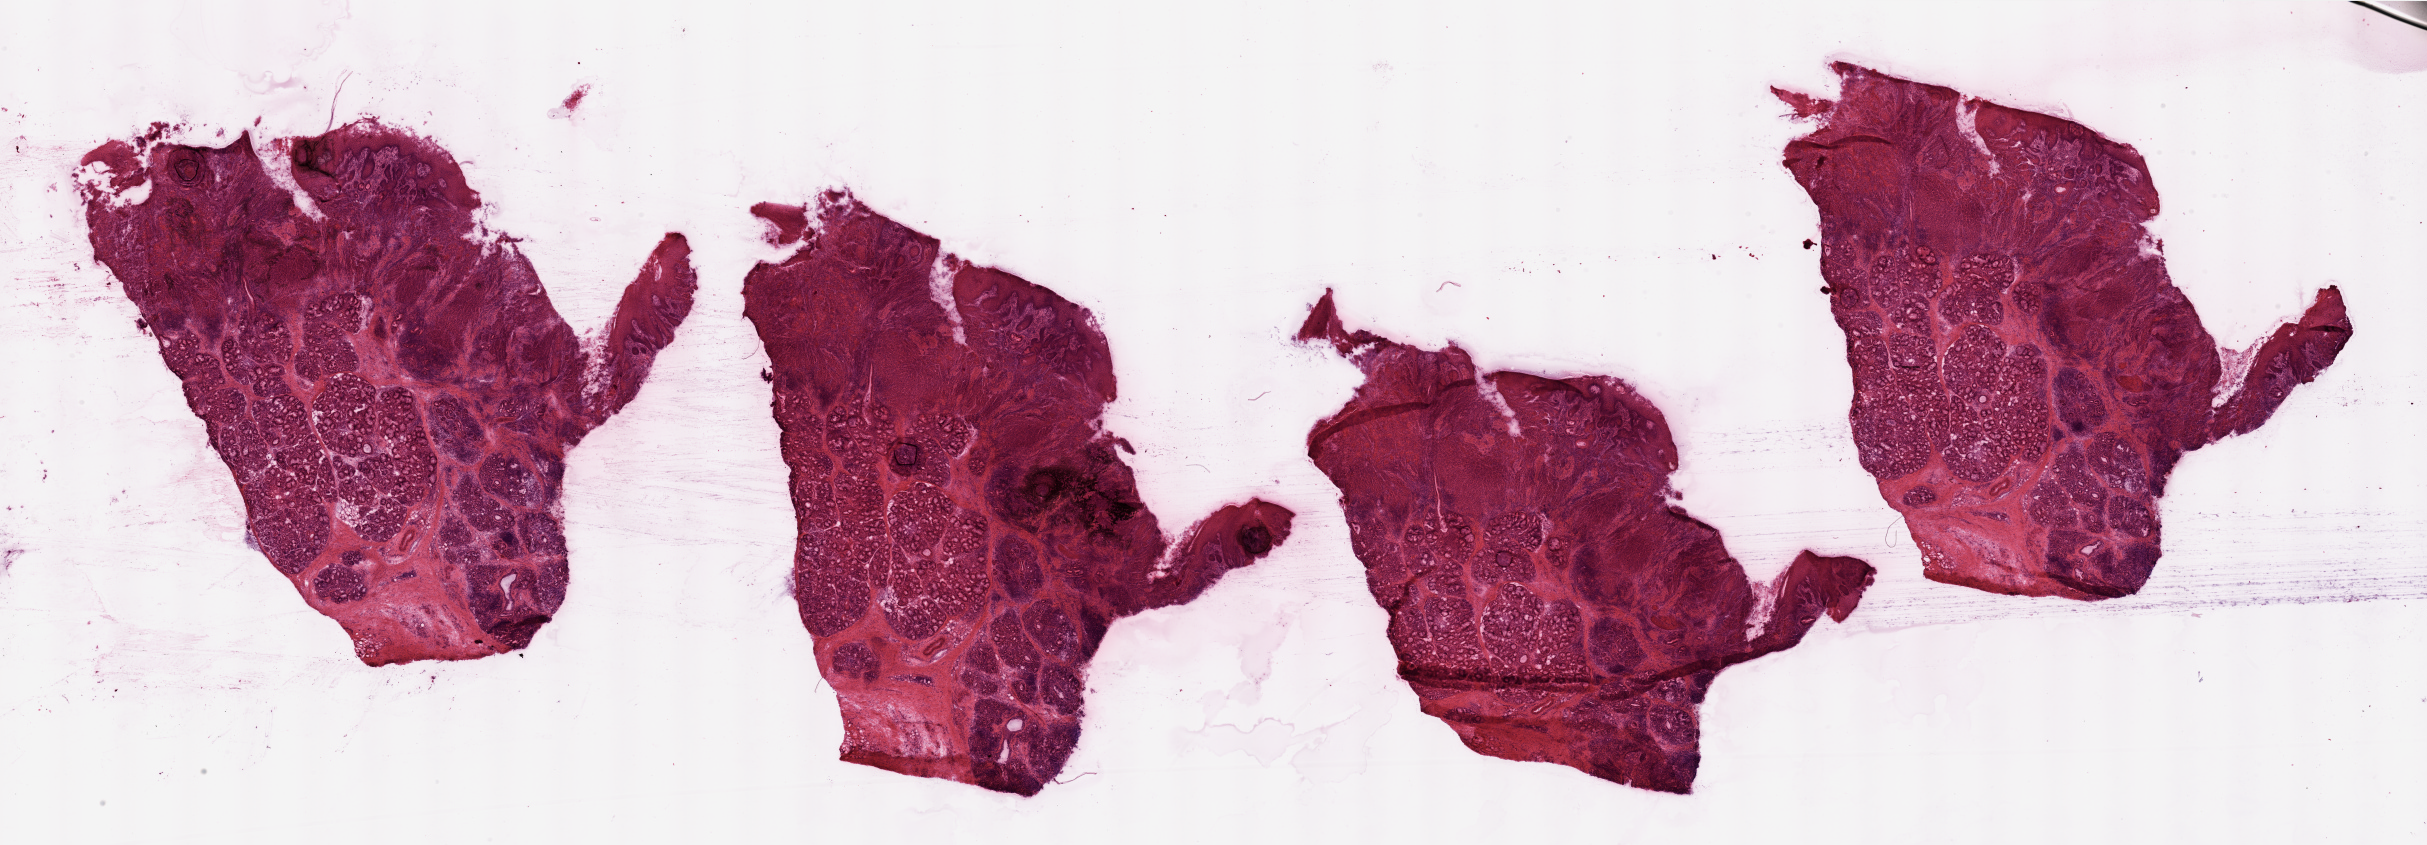
Whole-slide histology image, H&E-stained — whole scanned area (about 38.4 x 13.4 mm, acquisition: 20x scan) shown as a low-resolution overview. Head and neck, tissue type not recorded. Male, 50 y/o.
Patient diagnosis: Squamous cell carcinoma, NOS (larynx, NOS).